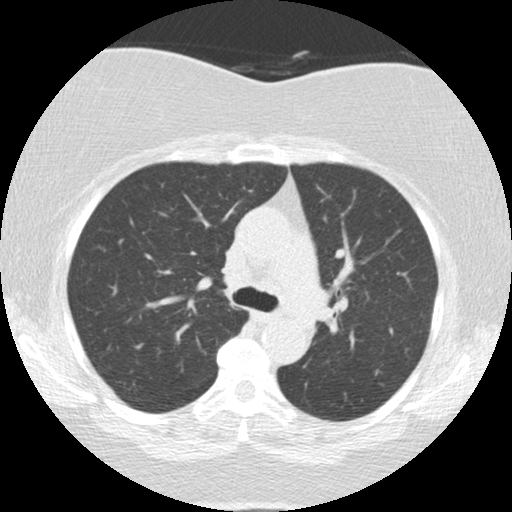
Low-dose screening chest CT, one axial slice. Slice 89 of 136 in the series (ordered by position). Reconstruction kernel STANDARD. 120 kVp. Lung window (W 1500 / L -600 HU). 512 × 512 image matrix, field of view 309 × 309 mm.
Outlined on this slice (expert manual segmentation):
- lesion 2 (tumor, mediastinum): bounding box (x1, y1, x2, y2) in pixels: (304, 287, 330, 320)